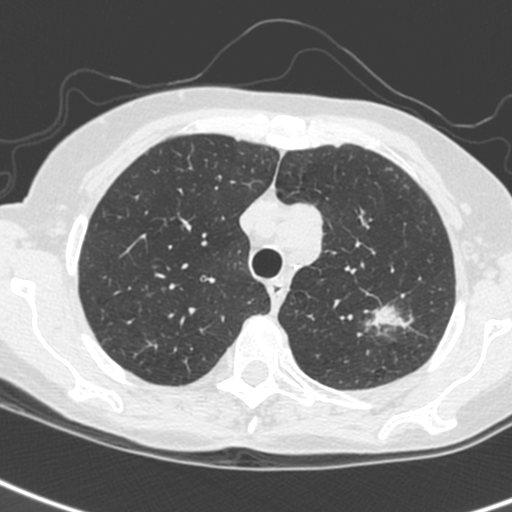
Chest CT (low-dose screening protocol), one axial image, baseline annual screen, lung window (W 1500 / L -600 HU), 1.3 mm slice thickness, standard (soft-tissue) reconstruction kernel (C), slice 44 of 242 in the series, 512 × 512 image matrix, field of view 284 × 284 mm. Female participant, aged 61 years at enrolment.
Lesion marked by an expert reader, bounding box (x1, y1, x2, y2) in pixels: (349, 298, 412, 349). The screening reader recorded 2 non-calcified nodules or masses ≥4 mm on this exam (left upper lobe, left upper lobe); which of them this box marks is not recorded. Official screen result: positive, change unspecified: nodule(s) >= 4 mm or enlarging nodule(s), mass(es), or other non-specific abnormalities suspicious for lung cancer. Later outcome: lung cancer diagnosed 29 days after this screen — small cell carcinoma, NOS, left upper lobe, stage IV (AJCC 6th edition).